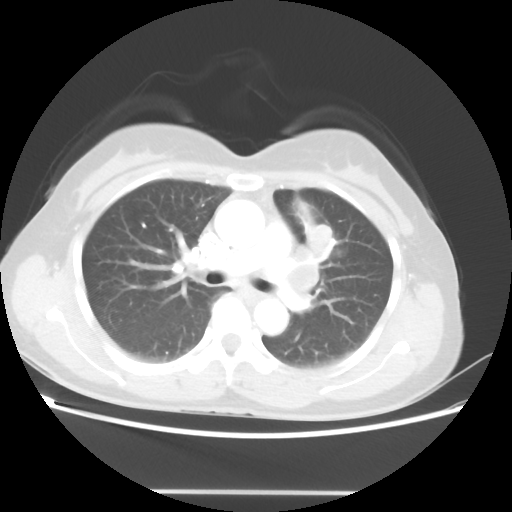
Chest CT, one axial slice. Slice 28 of 46 in the series (ordered by position). Reconstruction kernel STANDARD. 100 kVp. Lung window (W 1500 / L -600 HU). 5 mm slice thickness. 512 × 512 image matrix, field of view 360 × 360 mm. Female patient, age 50 years. From the clinical record (not read from this slice): clinical TNM (as recorded): T1c N1 M0; histopathological grade: G3.
Outlined on this slice (rectangle marked by the reading radiologist):
- lung tumour (recorded histology: adenocarcinoma): bounding box <299,216,333,257> (left, top, right, bottom; pixels)